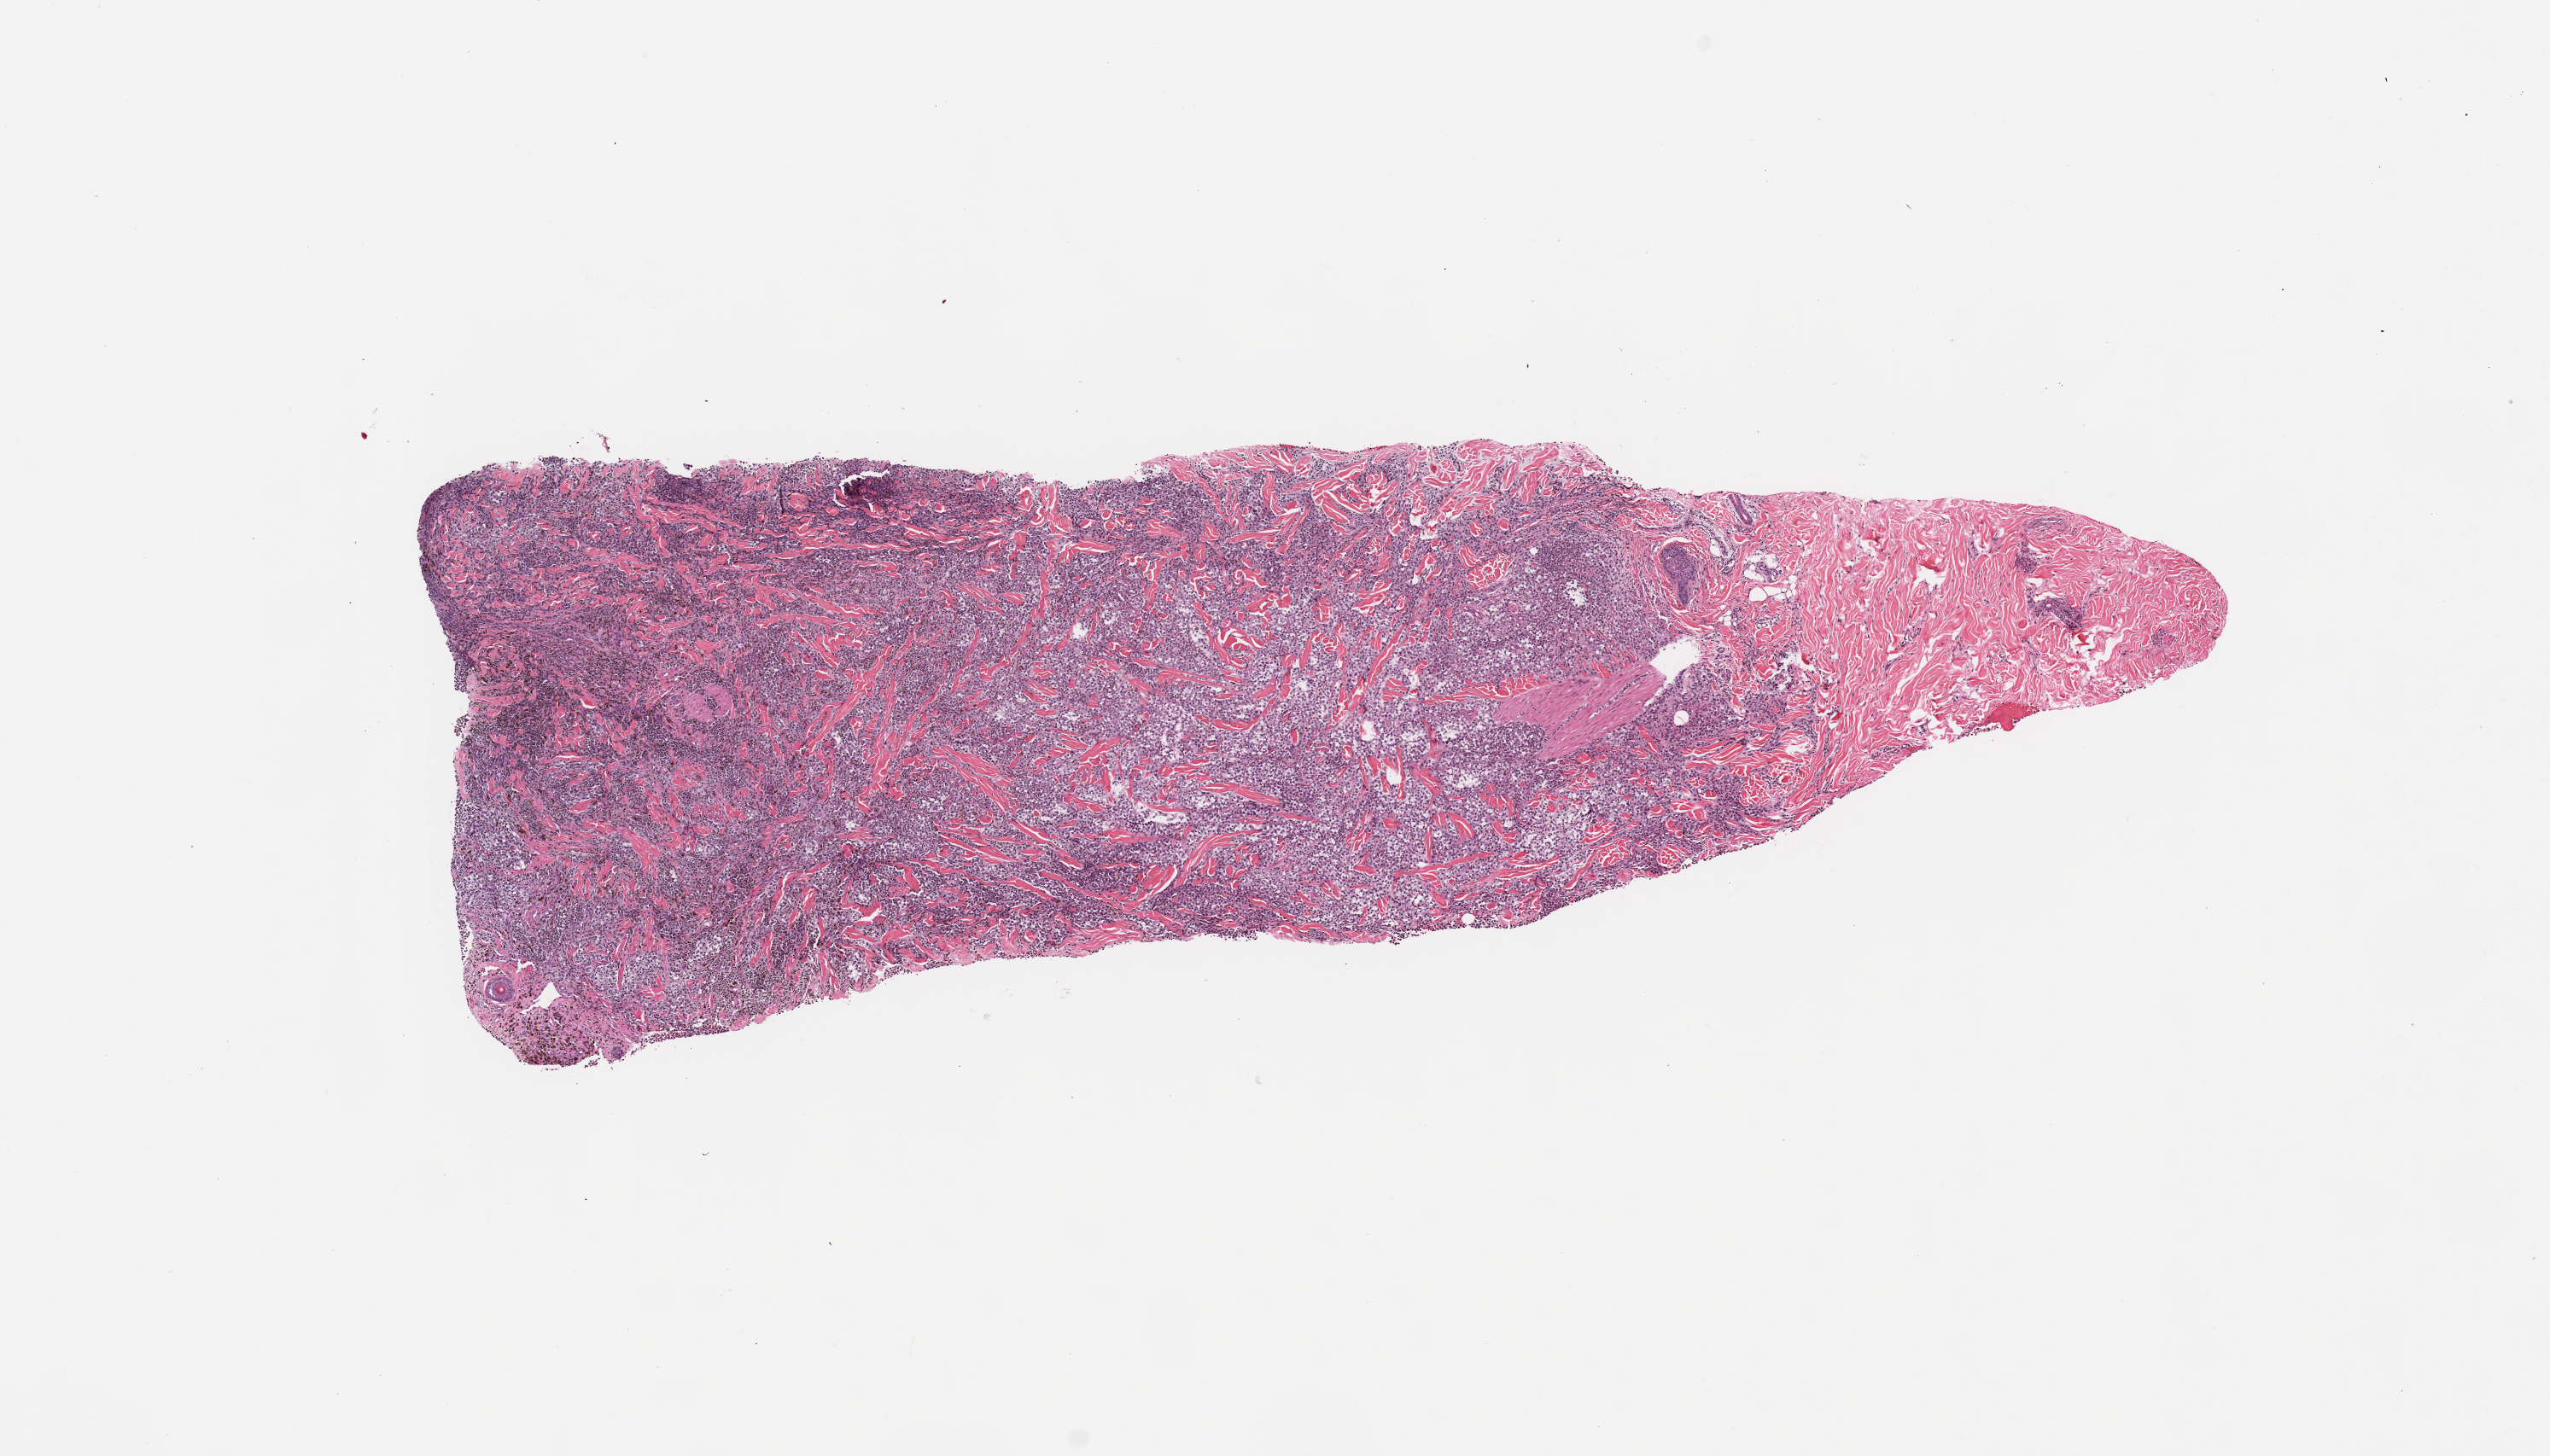
Whole-slide histology image, Hematoxylin and eosin (H&E) stained, whole scanned area (about 11.8 x 6.7 mm, slide scanned at 20x) shown as a low-resolution overview; tumour tissue sample, sampled site: trunk. Female, 69 y/o. Pathologist review of this section (percent, as recorded): tumour nuclei 90%, necrosis 0%.
* histologic diagnosis: Malignant melanoma, NOS
* primary tumour site (as recorded): trunk
* AJCC pathologic stage: IIIB